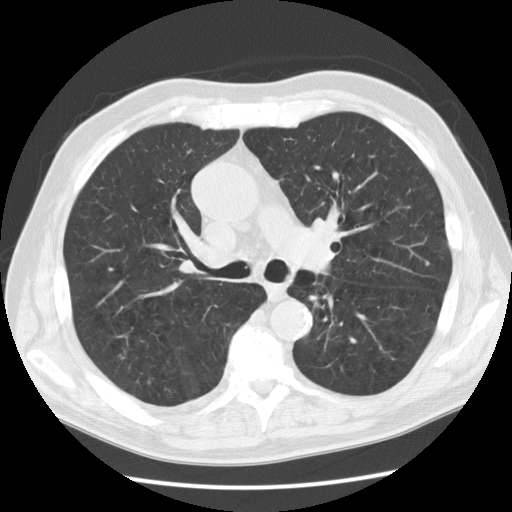
Low-dose screening chest CT, one axial slice. Slice 81 of 130 in the series (ordered by position). Reconstruction kernel STANDARD. Lung window (W 1500 / L -600 HU). 2.5 mm slice thickness. 512 × 512 image matrix.
Structures marked on this image (manually delineated by an expert):
- lesion 1 (tumor, lower lobe of left lung): bounding box <307,285,329,308> (left, top, right, bottom; pixels)